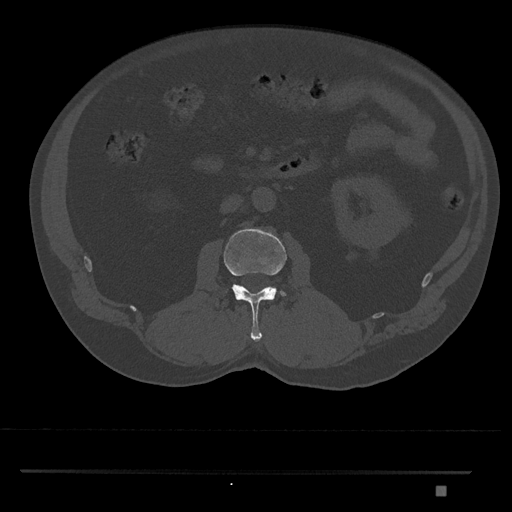
CT including the spine, one axial slice; slice 744 of 1134 in the series (ordered by position); 120 kVp; bone window (W 1800 / L 400 HU); 512 × 512 image matrix, field of view 429 × 429 mm. Male patient, age 65 years. From the clinical record (not read from this slice): primary cancer: prostate.
Annotated regions visible in this slice (semi-automatic segmentation, software-assisted and operator-edited):
- L2 vertebra: box from (x=224, y=228) to (x=287, y=342) px